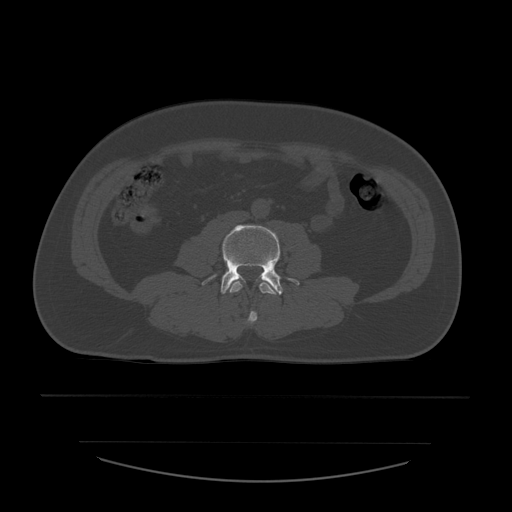
CT including the spine, one axial slice; bone window (W 1800 / L 400 HU); 512 × 512 image matrix, field of view 441 × 441 mm. Patient age 44 years. Case-level facts recorded for this patient, not image findings: primary cancer: soft tissue sarcoma.
Outlined on this slice (semi-automatic segmentation, software-assisted and operator-edited):
- L3 vertebra: bounding box <230,281,277,324> (left, top, right, bottom; pixels)
- L4 vertebra: <202,225,300,295>